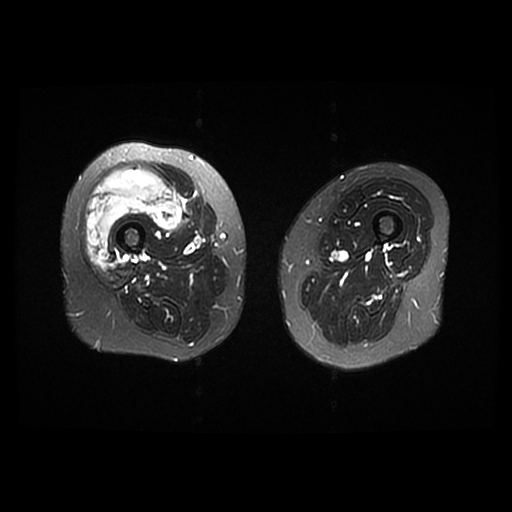
MRI of an extremity soft-tissue mass, one axial slice. Slice 14 of 42 in the series (ordered by position). T2-weighted fat-saturated. 6 mm slice thickness. 512 × 512 image matrix, field of view 440 × 440 mm. Female patient. From the clinical record (not read from this slice): histological type: pleiomorphic undifferentiated sarcoma; grade: high; site of the primary tumour: right quadricep.
Structures marked on this image (outlined manually by an expert reader):
- gross tumour volume including surrounding oedema: bounding box <86,167,181,263> (left, top, right, bottom; pixels)
- gross tumour volume (mass): <86,167,181,263>